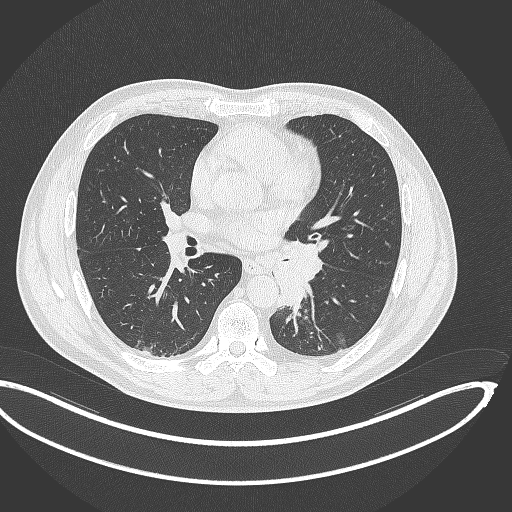
Chest CT, one axial slice; slice 181 of 362 in the series (ordered by position); lung window (W 1500 / L -600 HU); 1 mm slice thickness; 512 × 512 image matrix, field of view 442 × 442 mm. Patient: male, 50 years. Case-level facts recorded for this patient, not image findings: clinical TNM (as recorded): T2a N3 M0.
Outlined on this slice (rectangle marked by the reading radiologist):
- lung tumour (recorded histology: squamous cell carcinoma): bounding box (x1, y1, x2, y2) in pixels: (266, 249, 324, 310)